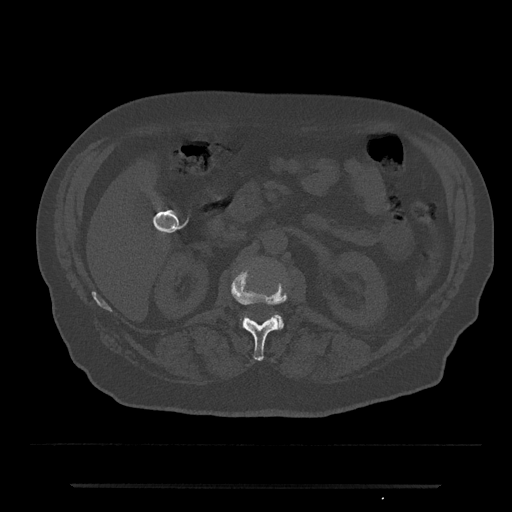
CT including the spine, one axial slice; reconstruction kernel Br40s/3; 120 kVp; bone window (W 1800 / L 400 HU); 512 × 512 image matrix, field of view 434 × 434 mm. Male patient, age 80 years. Case-level facts recorded for this patient, not image findings: primary cancer: prostate; vertebrae with lytic lesions (as recorded): L1, T11.
Annotated regions visible in this slice (semi-automatic segmentation, software-assisted and operator-edited):
- L1 vertebra: bounding box [x1, y1, x2, y2] px = [232, 272, 287, 361]
- L2 vertebra: [243, 314, 284, 330]